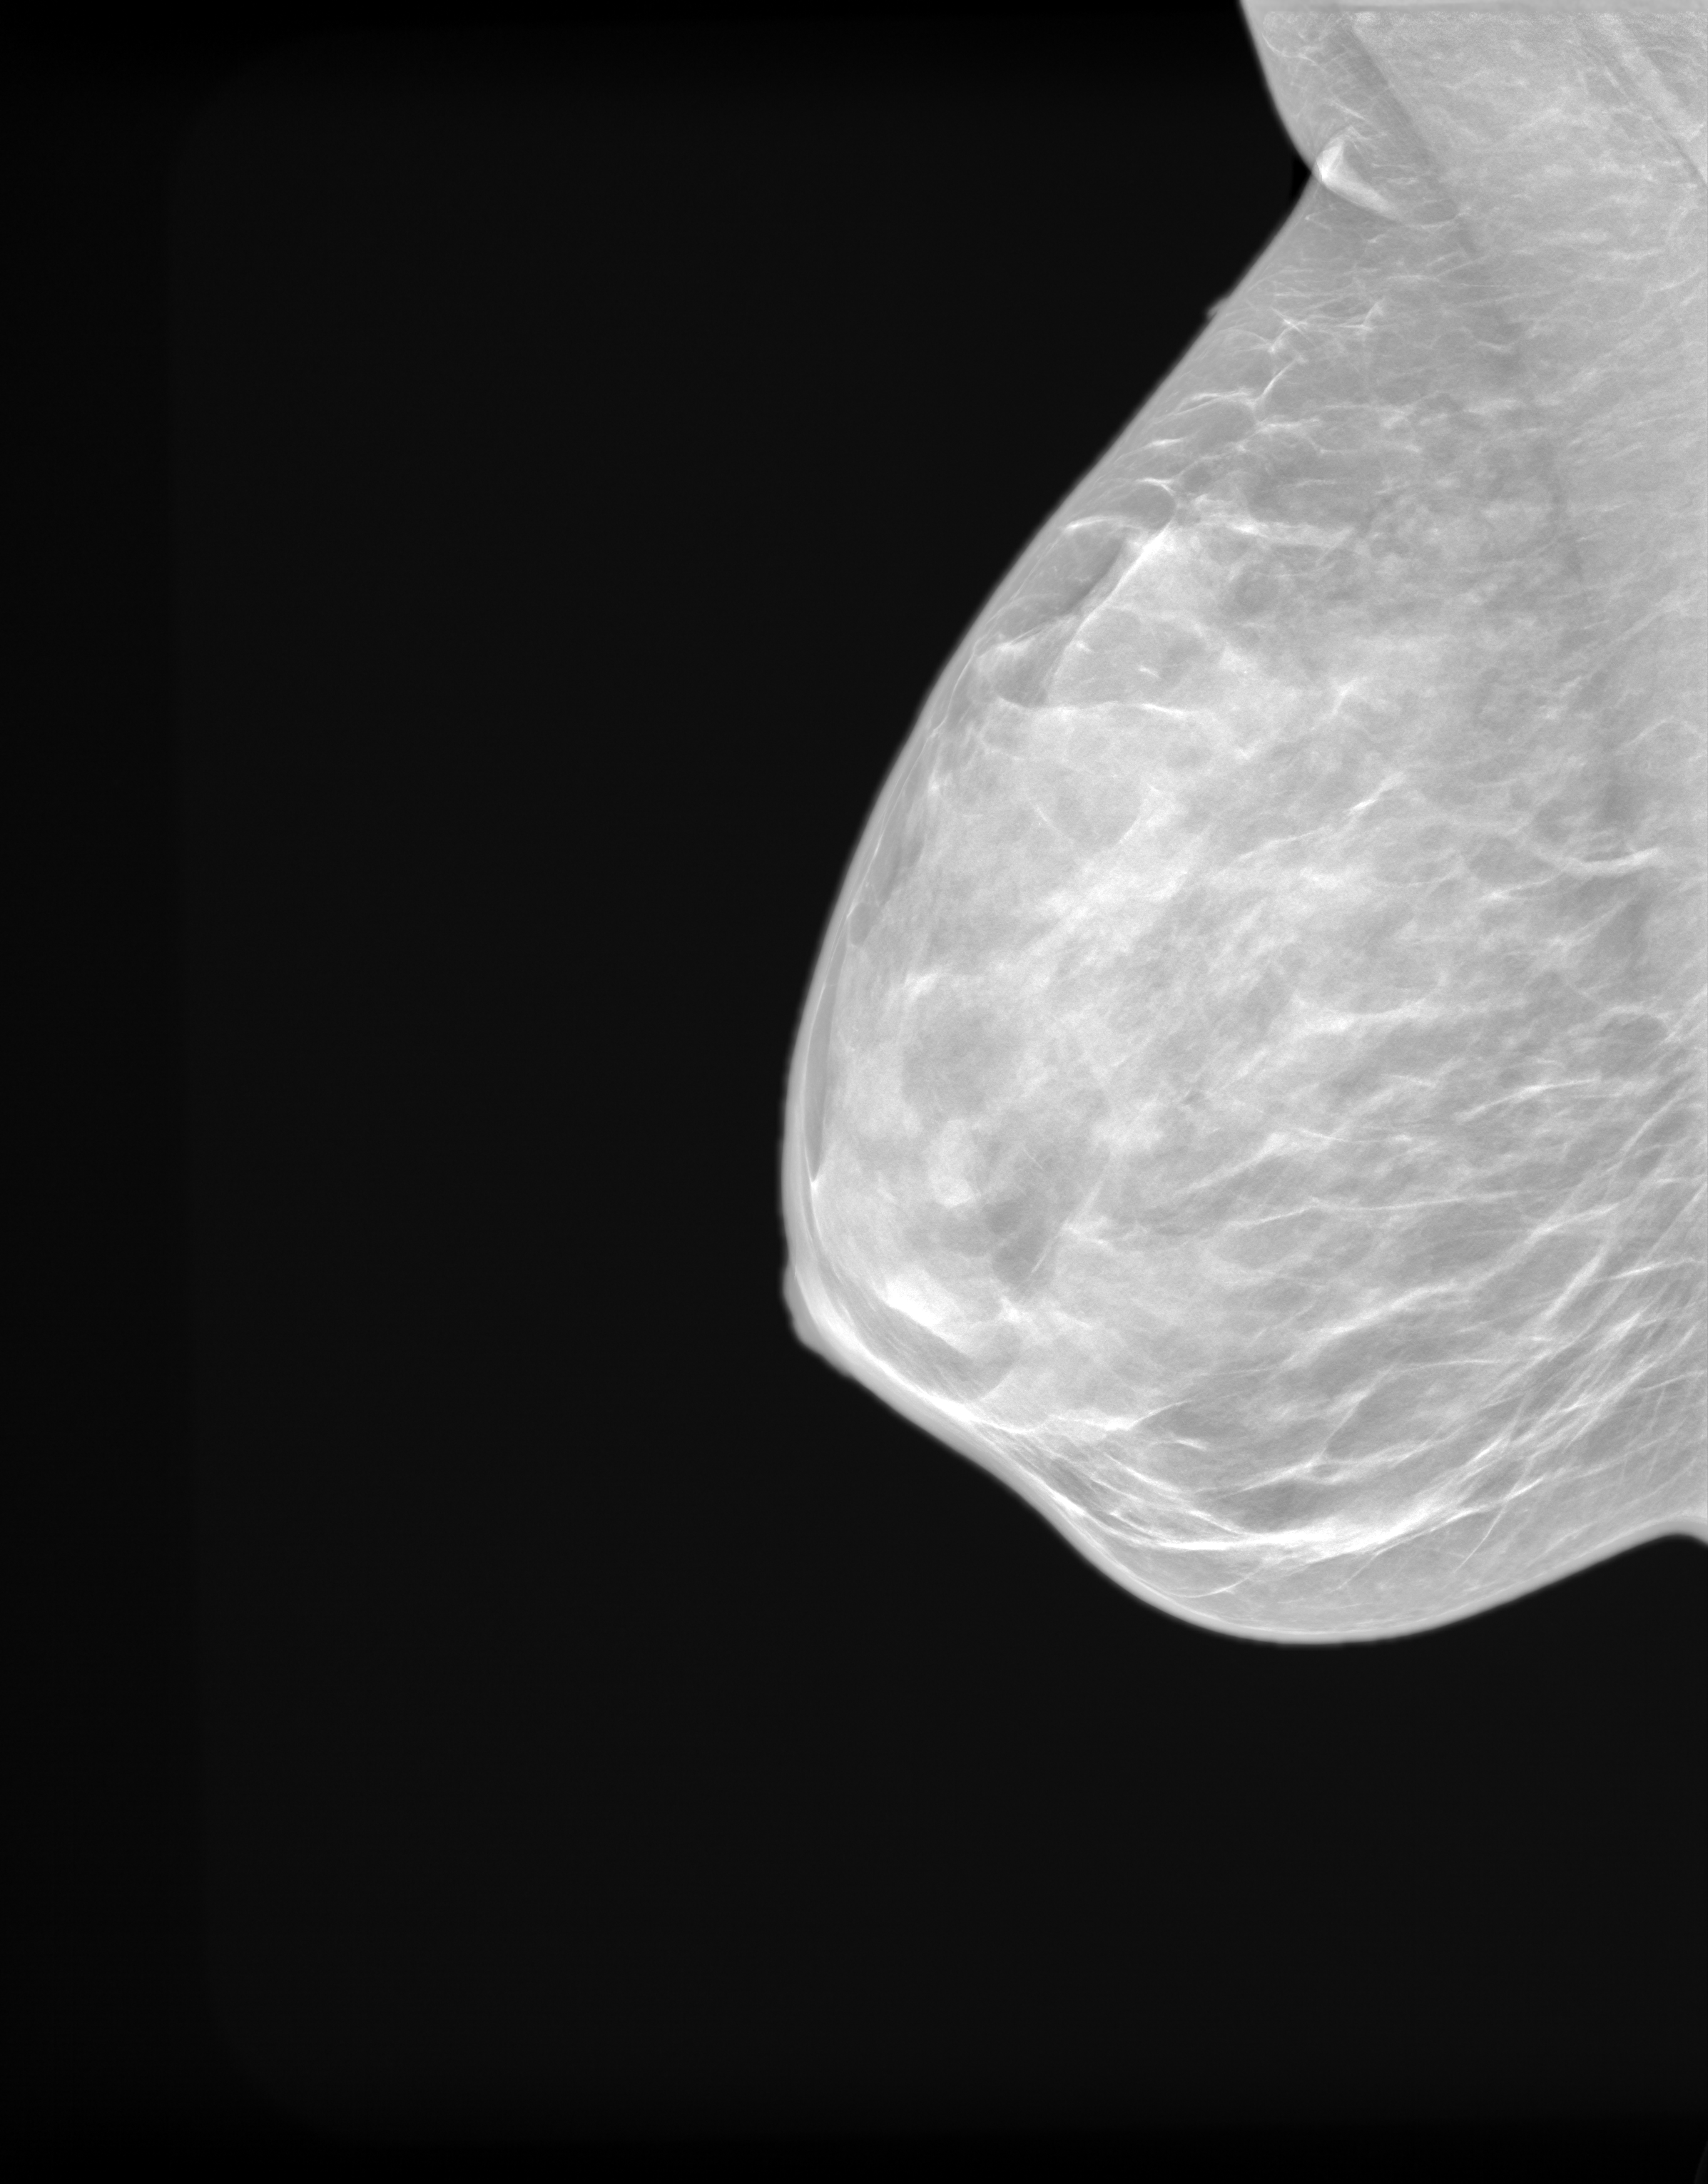
Screening examination. Patient aged 48 years (female).
Image type: synthesized 2-D view from tomosynthesis. Breast: right. Projection: mediolateral oblique (MLO) view. BI-RADS breast density category at the screening exam (both breasts, scale 1–4): 4. Final BI-RADS assessment for this screening round (tomosynthesis exam, both breasts): category 2. Recall: recalled for additional imaging after this screen.